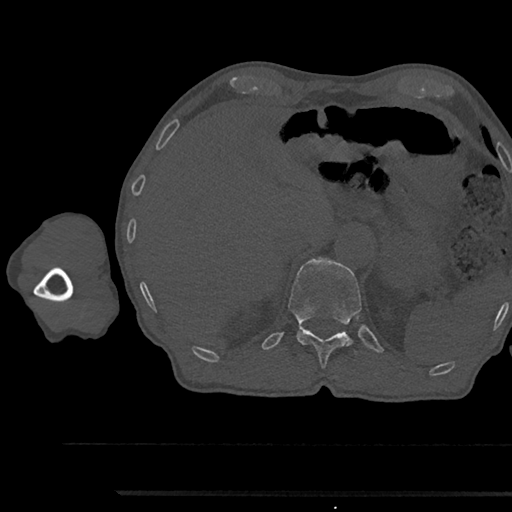
CT including the spine, one axial slice; slice 709 of 797 in the series (ordered by position); reconstruction kernel Br40s/3; bone window (W 1800 / L 400 HU); 0.5 mm slice thickness; 512 × 512 image matrix, field of view 367 × 367 mm. Male patient, age 79 years. Case-level facts recorded for this patient, not image findings: primary cancer: prostate.
Annotated regions visible in this slice (semi-automatically segmented with operator editing):
- T12 vertebra: box from (x=289, y=258) to (x=362, y=369) px